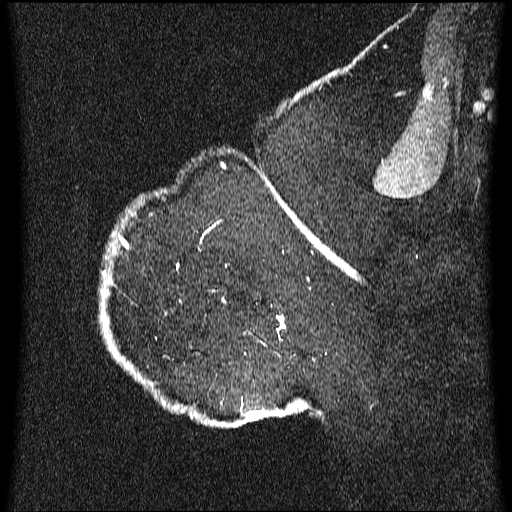
Breast MRI (dynamic contrast-enhanced), one sagittal slice. Position 50 of 64 along the scan axis. Dynamic contrast-enhanced series, image 2 of 3 at this slice position (ordered by acquisition). 1.5 T. TE 4.2 ms, TR 9.1 ms. 2.2 mm slice thickness. 512 × 512 image matrix, field of view 180 × 180 mm. Patient: female, 52 years.
Structures marked on this image (semi-automatically segmented with operator editing):
- analysis volume of interest (the breast-tissue region the enhancement analysis was run in; not a lesion): bounding box (x1, y1, x2, y2) in pixels: (100, 203, 350, 429)
- tumour enhancement mask (voxels above the 70 % enhancement threshold inside the analysis volume of interest): (104, 204, 350, 425)